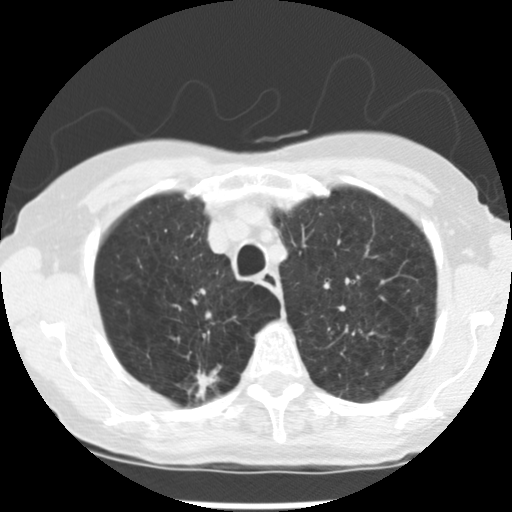
Axial slice from a low-dose chest CT screening exam, baseline annual screen, lung window (W 1500 / L -600 HU), slice 48 of 265 in the series, 512 × 512 image matrix, field of view 300 × 300 mm. Female, age 72 years at enrolment. Current smoker at enrolment.
Expert-annotated lung lesion, box from (x=183, y=362) to (x=233, y=406) px. The screening reader recorded 3 non-calcified nodules or masses ≥4 mm on this exam (right upper lobe, left upper lobe, left lower lobe); which of them this box marks is not recorded. Official screen result: positive, change unspecified: nodule(s) >= 4 mm or enlarging nodule(s), mass(es), or other non-specific abnormalities suspicious for lung cancer.